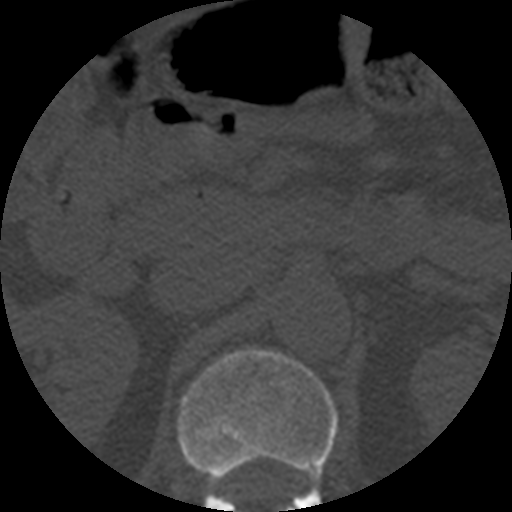
CT including the spine, one axial slice. Position 194 of 508 along the scan axis. 120 kVp. Bone window (W 1800 / L 400 HU). 1.25 mm slice thickness. 512 × 512 image matrix, field of view 160 × 160 mm. Patient age 57 years. Case-level facts recorded for this patient, not image findings: primary cancer: prostate.
Outlined on this slice (semi-automatic segmentation, software-assisted and operator-edited):
- L1 vertebra: bounding box [x1, y1, x2, y2] px = [177, 349, 338, 512]